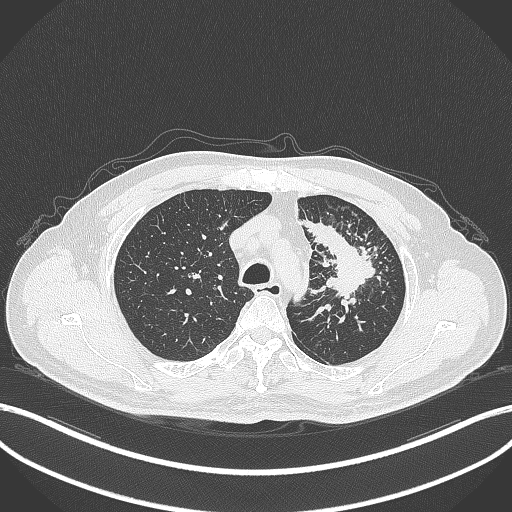
Chest CT, one axial slice; reconstruction kernel B70f; 120 kVp; lung window (W 1500 / L -600 HU); 1 mm slice thickness; 512 × 512 image matrix, field of view 400 × 400 mm. Patient: male, 69 years. Case-level facts recorded for this patient, not image findings: clinical TNM (as recorded): T2a N2 M0; histopathological grade: G2-3.
Annotated regions visible in this slice (bounding box drawn by a radiologist):
- lung tumour (recorded histology: adenocarcinoma): box from (x=303, y=216) to (x=380, y=303) px